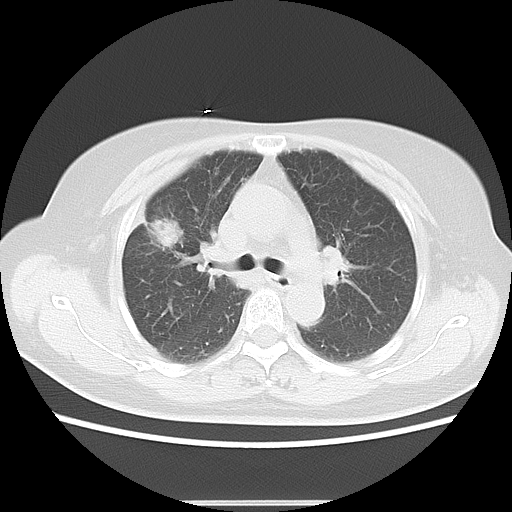
Chest CT, one axial slice; position 1 of 8 along the scan axis; reconstruction kernel LUNG; lung window (W 1500 / L -600 HU); 512 × 512 image matrix, field of view 350 × 350 mm. Patient: female, 57 years. From the clinical record (not read from this slice): clinical TNM (as recorded): T1c N1 M0.
Outlined on this slice (bounding box drawn by a radiologist):
- lung tumour (recorded histology: adenocarcinoma): bounding box [x1, y1, x2, y2] px = [148, 213, 188, 256]